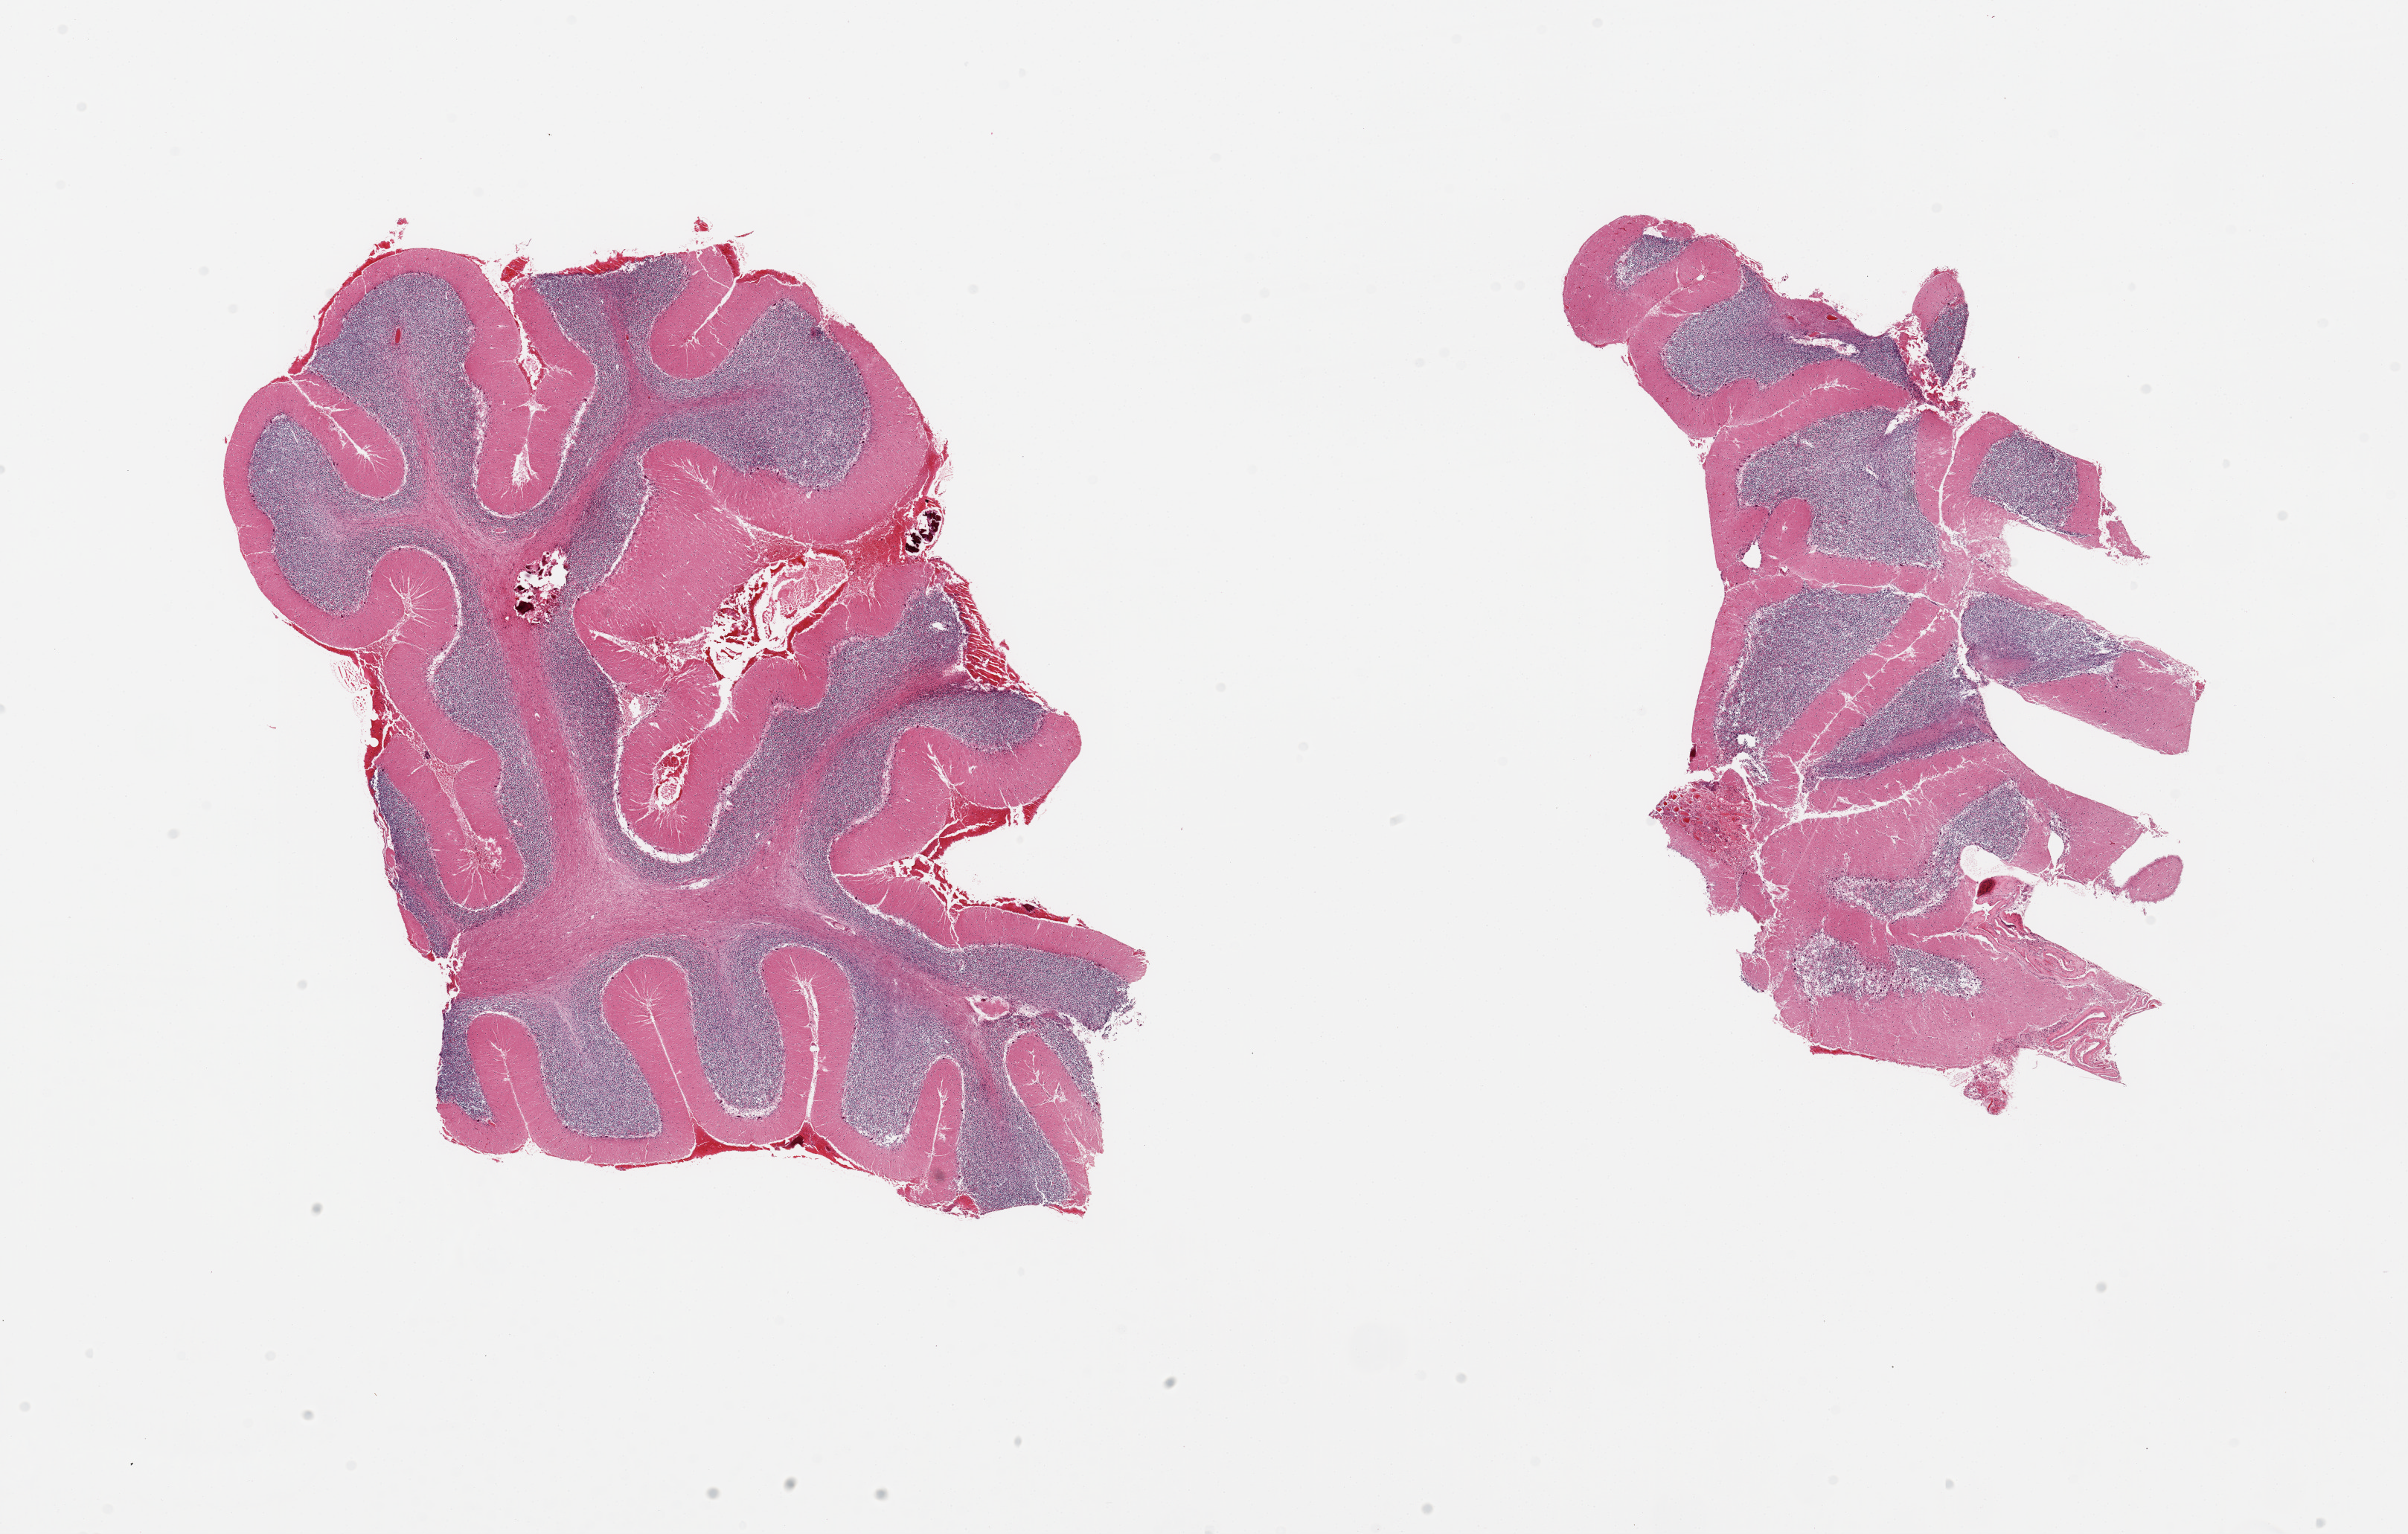
Whole-slide image, hematoxylin and eosin (H&E) stain, shown as a low-resolution overview of the whole scanned area (about 25.6 x 16.3 mm, slide scanned at 20x), PAXgene-fixed, paraffin-embedded tissue, sampled site (target tissue): cerebellum, tissue donor sample. Donor: male.
* pathologist's review note for this sample: 2 pieces; hemorrhage and bone fragments on surface